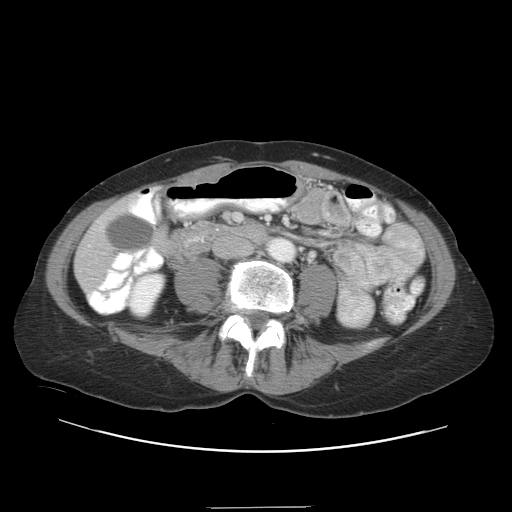
Contrast-enhanced abdominal CT, one axial slice. Position 4 of 38 along the scan axis. Reconstruction kernel STANDARD. Soft-tissue window (W 400 / L 40 HU). 5 mm slice thickness. 512 × 512 image matrix, field of view 388 × 388 mm. Female patient, age 64 years. Case-level facts recorded for this patient, not image findings: diagnosis: colorectal cancer liver metastases, imaged before liver resection; multiple liver metastases: no; largest metastasis: 3.8 cm; chemotherapy before resection: yes.
Outlined on this slice (outlined manually by an expert reader):
- liver: bounding box [x1, y1, x2, y2] px = [77, 208, 122, 287]